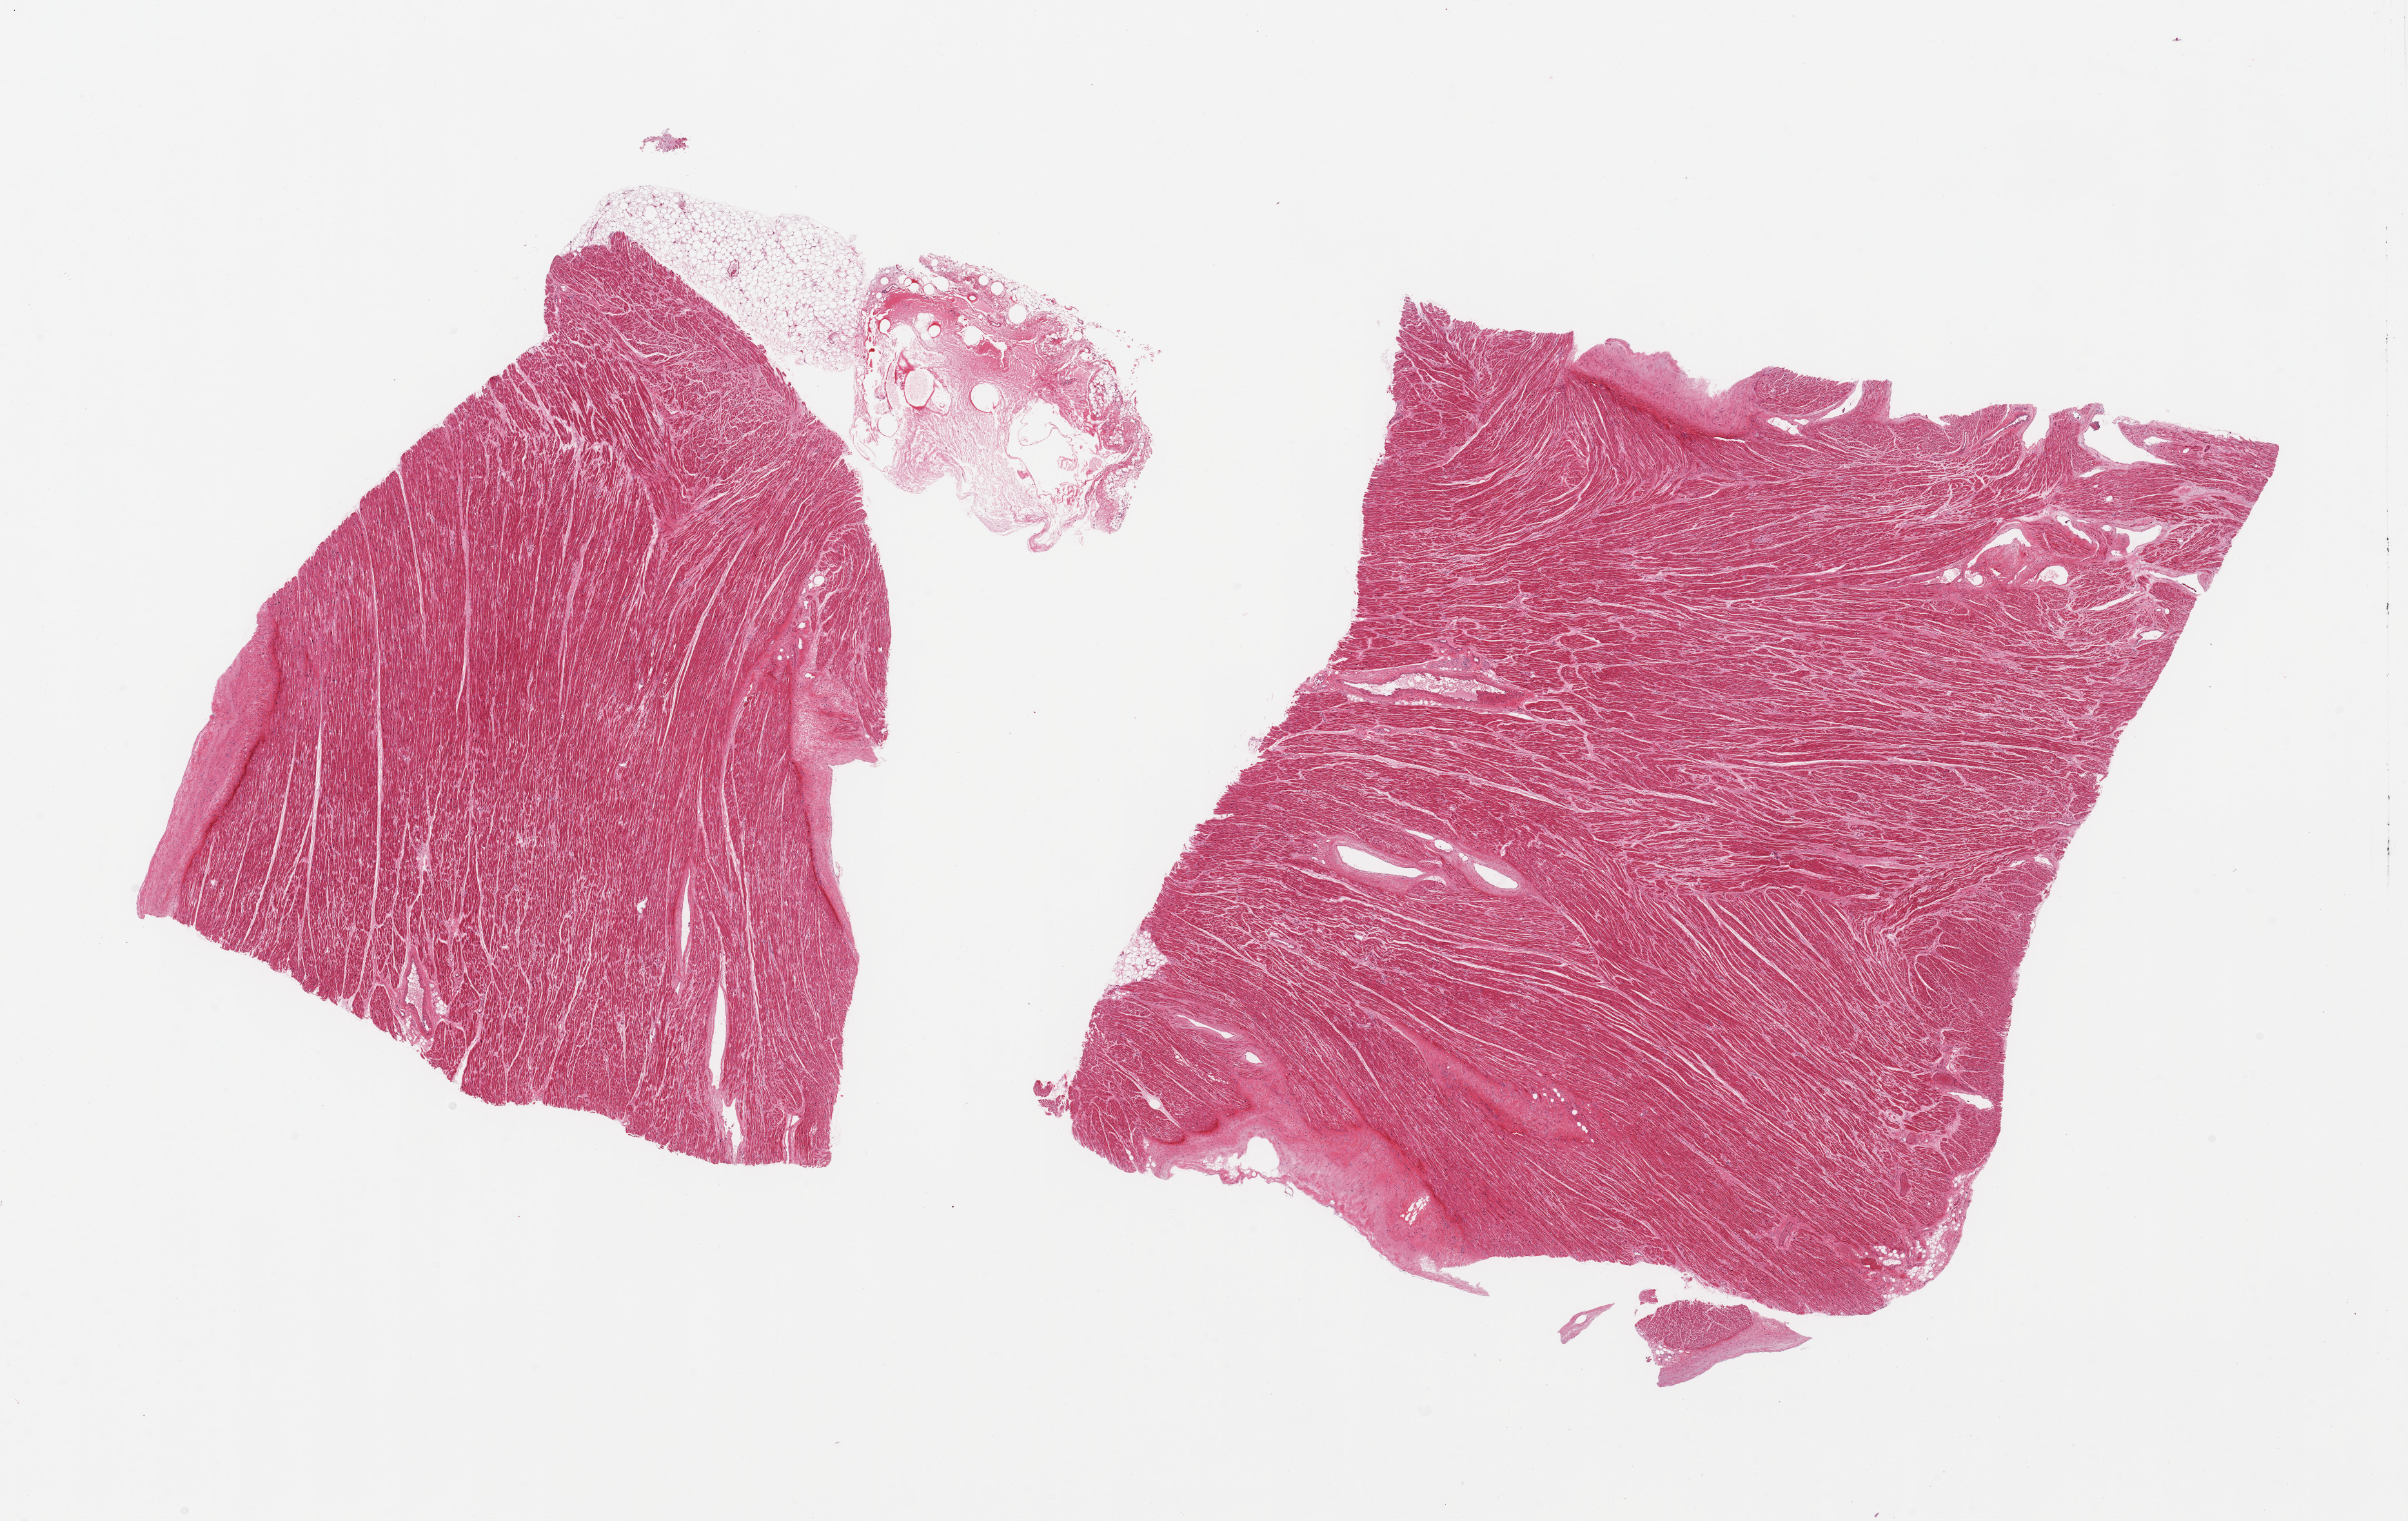
Whole-slide image, haematoxylin and eosin stain, brightfield, shown as a low-resolution overview of the whole scanned area (about 29.5 x 18.7 mm, acquisition: 20x scan). PAXgene-fixed paraffin-embedded (PFPE) section. Section of heart (target tissue). Tissue donor sample. Male donor.
Pathologist's review note for this sample: 2 pieces, moderate interstitial fibrosis/chronic ischemic change; ~7x2 mm adherent nubbin of epicardial fat.